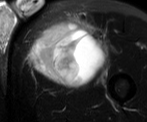
MRI of an extremity soft-tissue mass, one axial slice. Position 43 of 52 along the scan axis. T2-weighted fat-saturated. MR volume resampled by the dataset authors to the PET/CT grid (not the native acquisition matrix). 3.27 mm slice thickness. 147 × 122 image matrix. Male patient. Case-level facts recorded for this patient, not image findings: histological type: pleiomorphic liposarcoma; grade: high; site of the primary tumour: left thigh.
Structures marked on this image (expert contour drawn on MRI and transferred to this co-registered scan by the dataset authors):
- gross tumour volume including surrounding oedema: bounding box [x1, y1, x2, y2] px = [34, 18, 106, 81]
- gross tumour volume (mass): [34, 27, 99, 81]